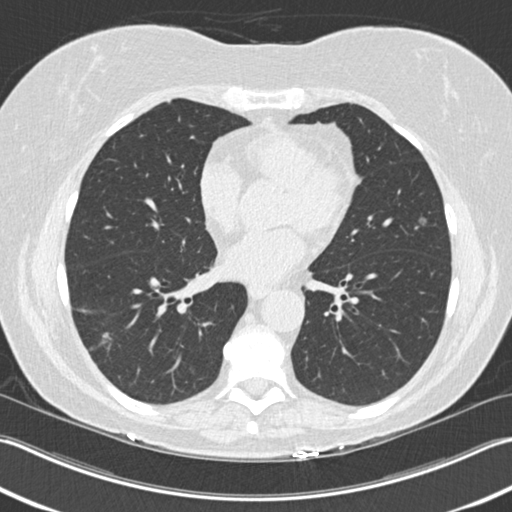
Chest CT (low-dose screening protocol), one axial image, baseline annual screen, lung window (W 1500 / L -600 HU). Female, age 63 years at enrolment. Current smoker at enrolment.
- Lesion marked by an expert reader, bounding box [x1, y1, x2, y2] px = [62, 304, 130, 369].
- The screening reader recorded 3 non-calcified nodules or masses ≥4 mm on this exam (right upper lobe, right lower lobe, right lower lobe); which of them this box marks is not recorded.